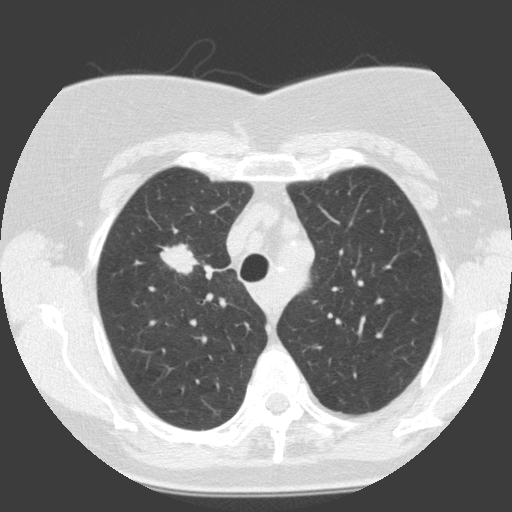
Low-dose screening chest CT, one axial slice; position 109 of 146 along the scan axis; 120 kVp; lung window (W 1500 / L -600 HU); 512 × 512 image matrix.
Outlined on this slice (manually delineated by an expert):
- lesion 1 (tumor, upper lobe of right lung): box from (x=160, y=243) to (x=195, y=275) px